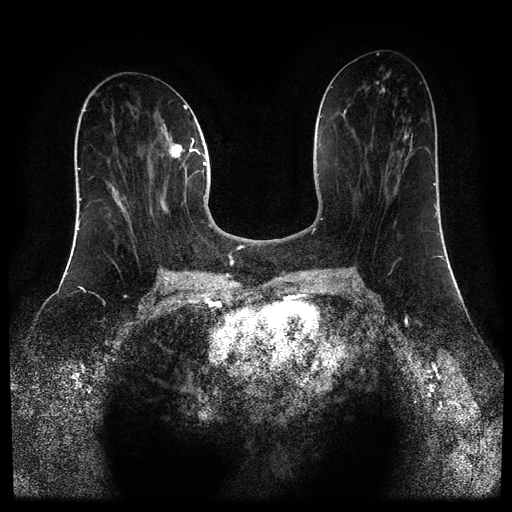
Breast MRI (dynamic contrast-enhanced, multi-phase), one axial slice. Dynamic contrast-enhanced series, time point 2 of 5 at this slice position (early post-contrast). 1.5 T. TE 2.6 ms, TR 5.4 ms. 512 × 512 image matrix. Patient: female, 43 years.
Structures marked on this image (semi-automatic segmentation, software-assisted and operator-edited):
- breast lesion (labelled 'tumour' in the annotation; benign lesions carry a separate 'benign' label): bounding box <160,144,183,213> (left, top, right, bottom; pixels)